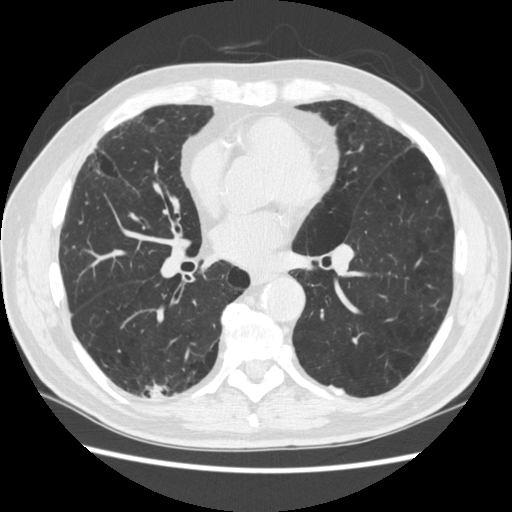
Low-dose screening chest CT, one axial slice. Position 128 of 266 along the scan axis. 120 kVp. Lung window (W 1500 / L -600 HU). 512 × 512 image matrix.
Annotated regions visible in this slice (outlined manually by an expert reader):
- lesion 1 (tumor, upper lobe of right lung): box from (x=151, y=385) to (x=163, y=399) px